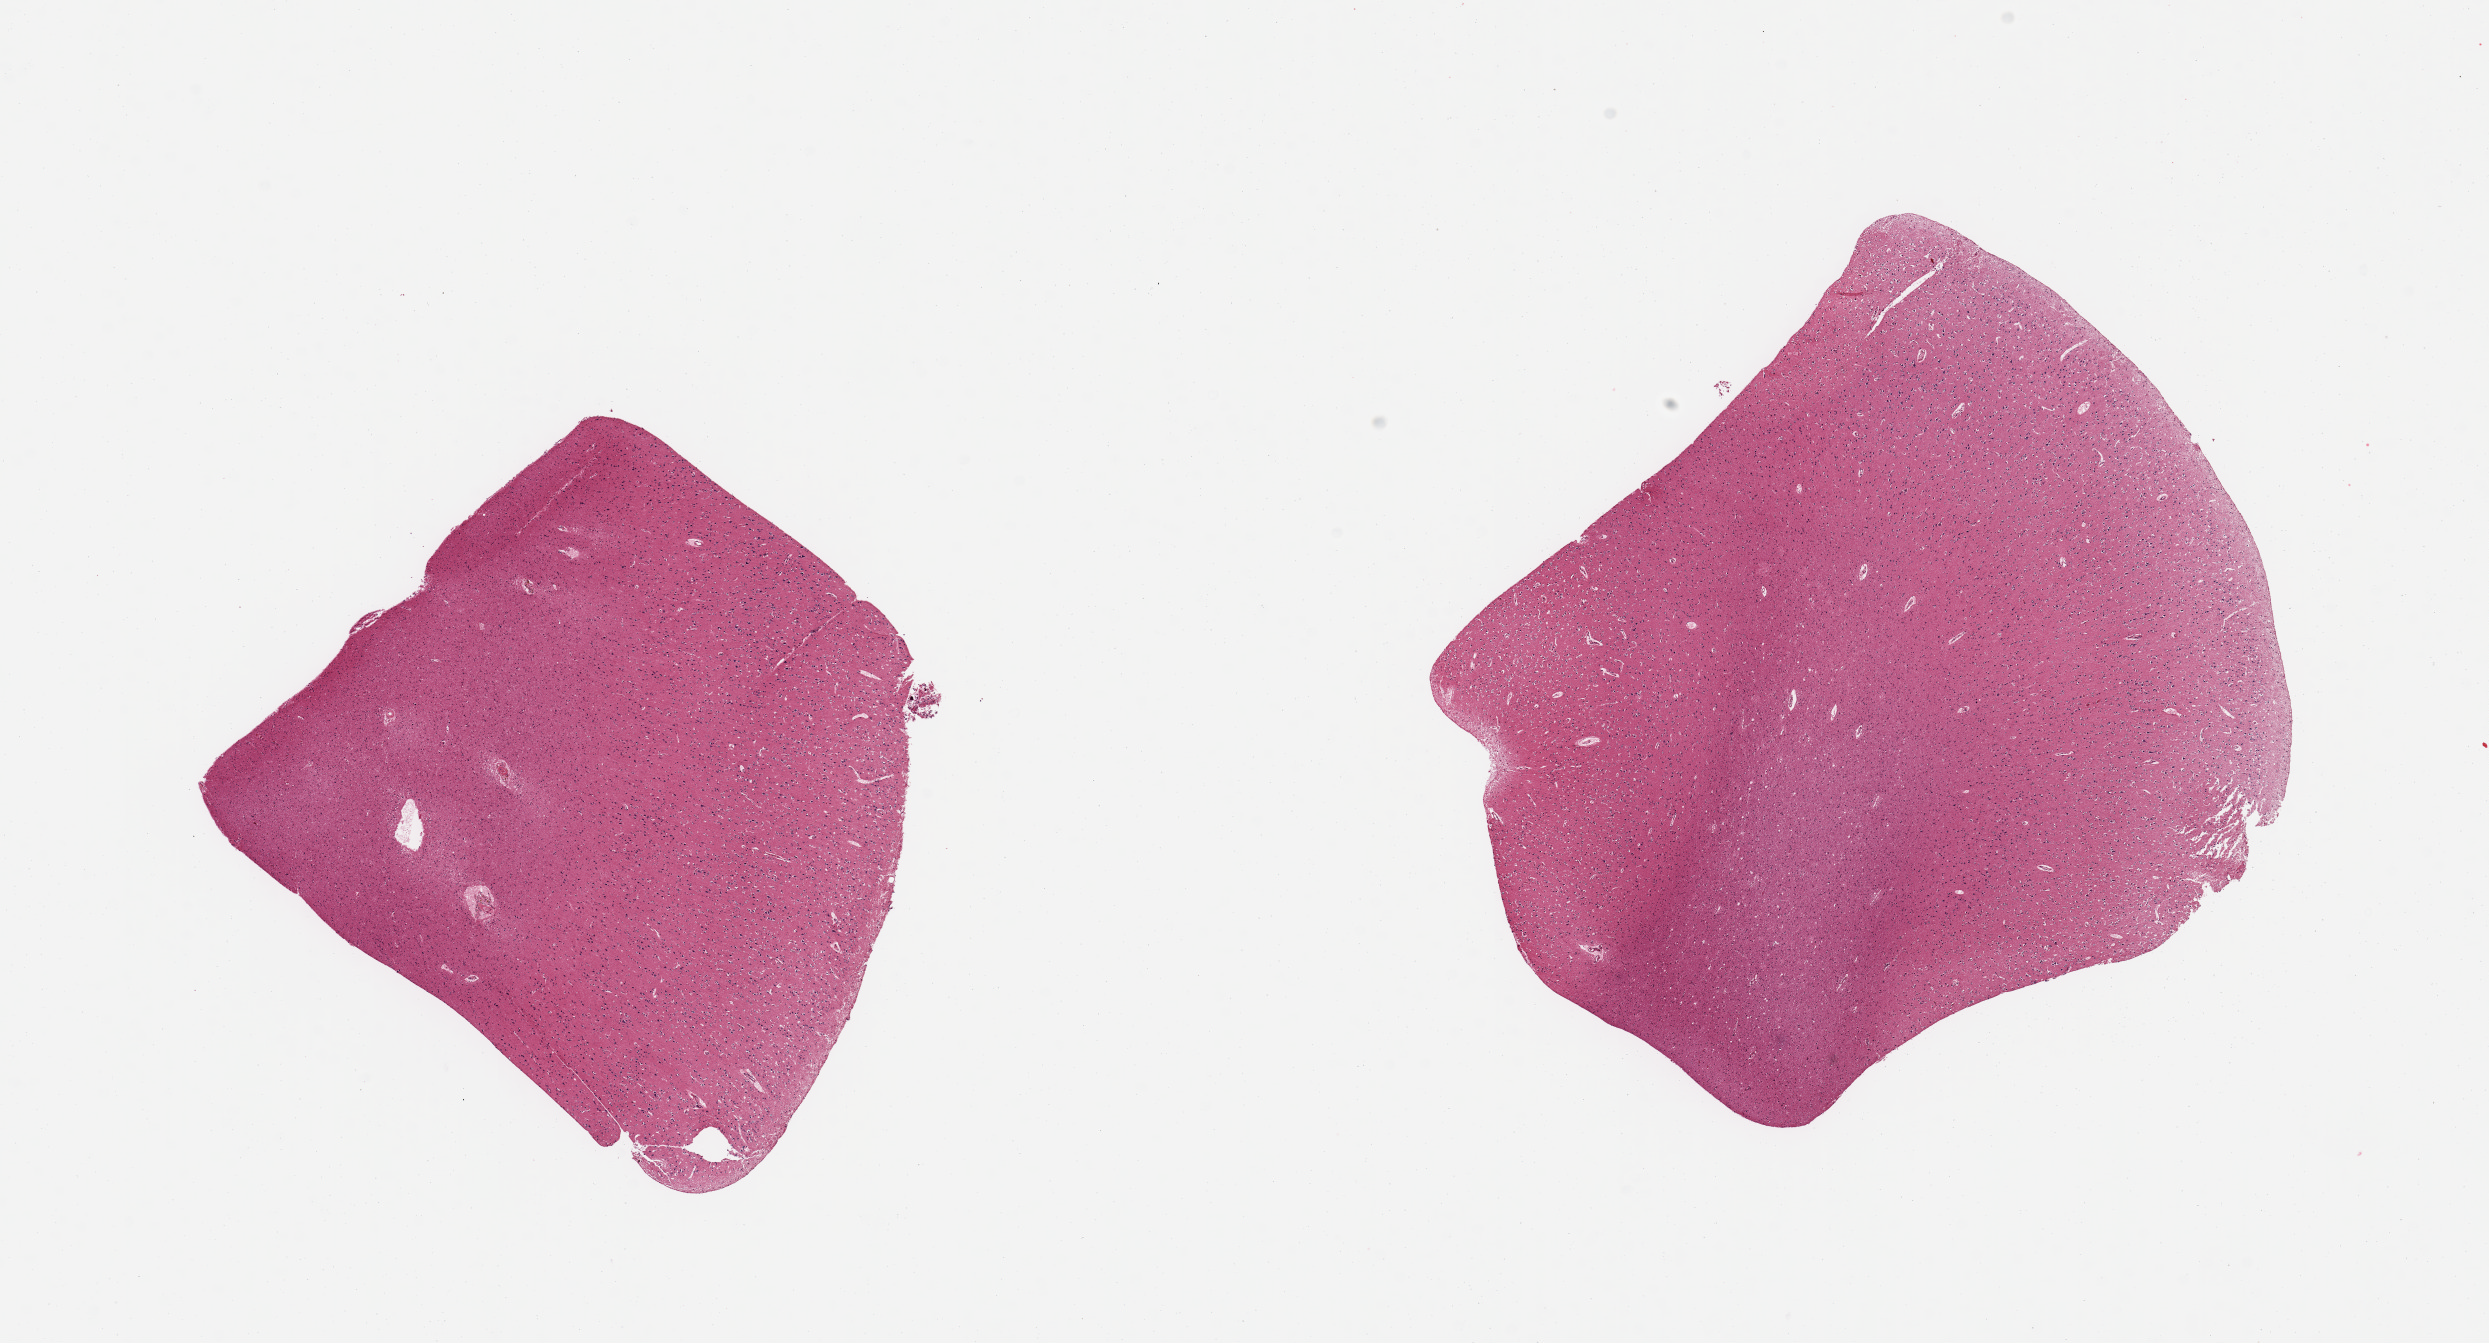
Whole-slide image, haematoxylin and eosin stain — a low-resolution overview of the entire scanned area, about 19.7 x 10.6 mm. PAXgene-fixed, paraffin-embedded tissue. Target tissue: cerebral cortex. Donor tissue sample. Donor: female.
Reviewer comment on this tissue sample: 2 pieces.